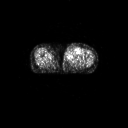
FDG PET of an extremity soft-tissue mass (from a PET/CT study), one axial slice; slice 45 of 91 in the series (ordered by position); 3.27 mm slice thickness; 128 × 128 image matrix, field of view 700 × 700 mm. Patient: female, 74 years. Case-level facts recorded for this patient, not image findings: histological type: pleomorphic leiomyosarcoma; grade: high; site of the primary tumour: left thigh.
Outlined on this slice (expert contour drawn on MRI and transferred to this co-registered scan by the dataset authors):
- gross tumour volume including surrounding oedema: bounding box [x1, y1, x2, y2] px = [65, 47, 79, 61]
- gross tumour volume (mass): [72, 52, 76, 54]